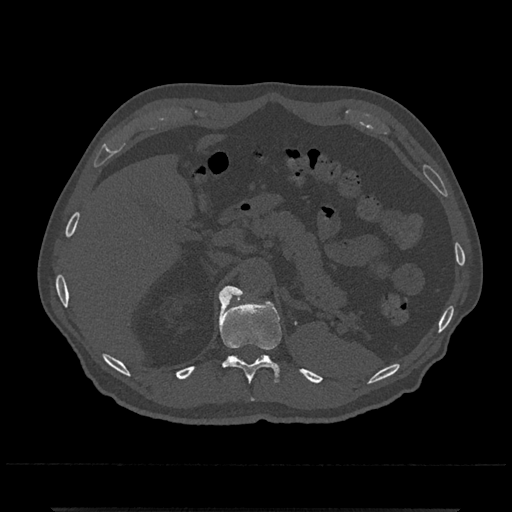
CT including the spine, one axial slice. Slice 482 of 797 in the series (ordered by position). 120 kVp. Bone window (W 1800 / L 400 HU). 0.5 mm slice thickness. 512 × 512 image matrix, field of view 393 × 393 mm. Male patient, age 67 years. From the clinical record (not read from this slice): primary cancer: prostate.
Annotated regions visible in this slice (semi-automatic segmentation, software-assisted and operator-edited):
- T11 vertebra: bounding box (x1, y1, x2, y2) in pixels: (218, 293, 282, 401)
- T12 vertebra: (221, 286, 243, 298)